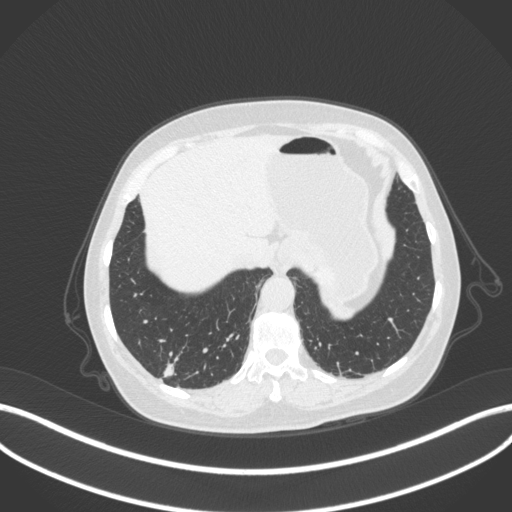
Chest CT, one axial slice. Slice 46 of 340 in the series (ordered by position). 120 kVp. Lung window (W 1500 / L -600 HU). 1 mm slice thickness. 512 × 512 image matrix. Patient: female, 69 years. Case-level facts recorded for this patient, not image findings: clinical TNM (as recorded): T1b N0 M0; histopathological grade: G2-3.
Annotated regions visible in this slice (rectangle marked by the reading radiologist):
- lung tumour (recorded histology: adenocarcinoma): bounding box <159,361,181,379> (left, top, right, bottom; pixels)